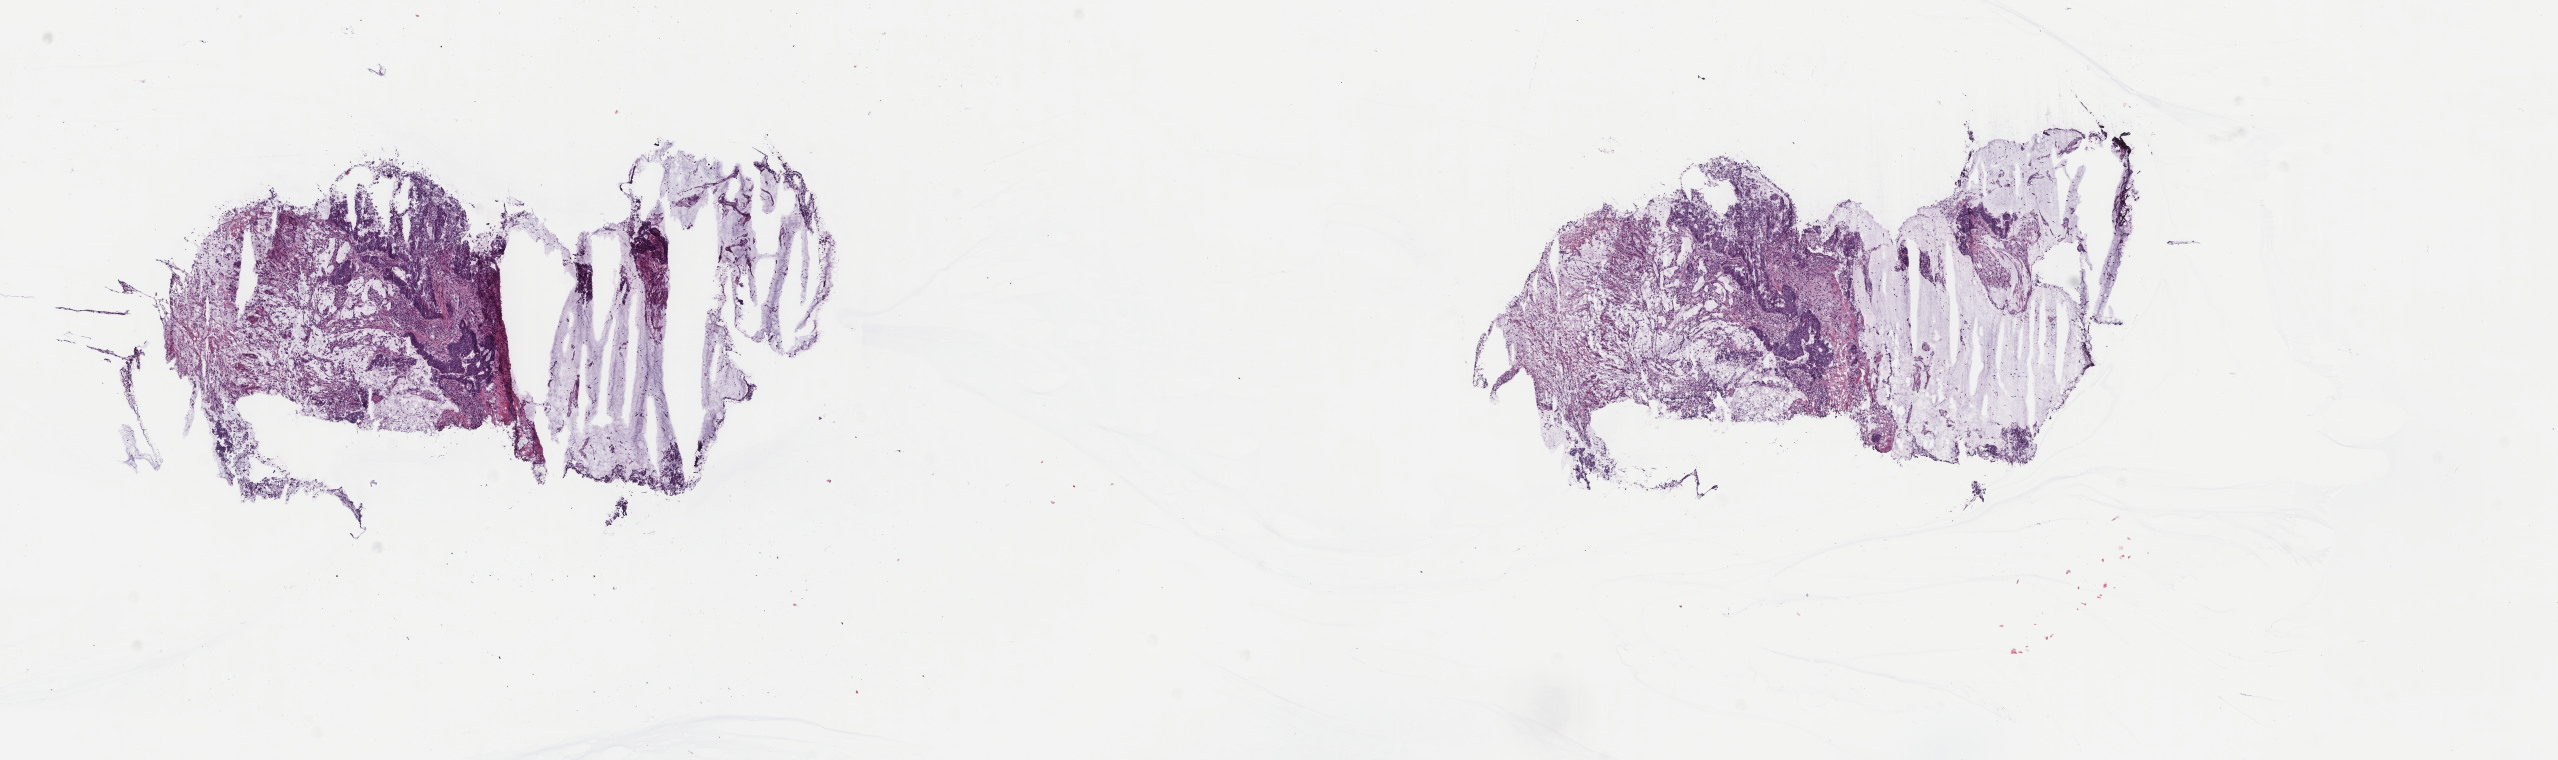
Digitized H&E tissue section (whole slide), a low-resolution overview of the entire scanned area, about 20.3 x 6.0 mm (from a 40x scan); frozen section; colon, primary tumour sample. Patient: female, age at initial diagnosis 55 years. Pathologist review of this section (percent, as recorded): tumour cells 45%, tumour nuclei 80%, normal cells 0%, stromal cells 35%, necrosis 20%. Infiltration values recorded for this section: lymphocyte infiltration 10%, monocyte infiltration 3%, neutrophil infiltration 2%.
TNM: T4 N1 M0. AJCC pathologic stage: IIIB (6th edition). Lymph nodes positive (case pathology): 2 of 13 examined. Pathologic diagnosis: Mucinous adenocarcinoma (descending colon).